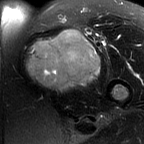
MRI of an extremity soft-tissue mass, one axial slice; slice 44 of 60 in the series (ordered by position); T2-weighted fat-saturated; MR volume resampled by the dataset authors to the PET/CT grid (not the native acquisition matrix); 3.27 mm slice thickness; 144 × 144 image matrix. Female patient. Case-level facts recorded for this patient, not image findings: histological type: pleiomorphic leiomyosarcoma; grade: intermediate; site of the primary tumour: left thigh.
Annotated regions visible in this slice (expert contour drawn on MRI and transferred to this co-registered scan by the dataset authors):
- gross tumour volume including surrounding oedema: bounding box (x1, y1, x2, y2) in pixels: (25, 28, 99, 91)
- gross tumour volume (mass): (25, 28, 99, 91)